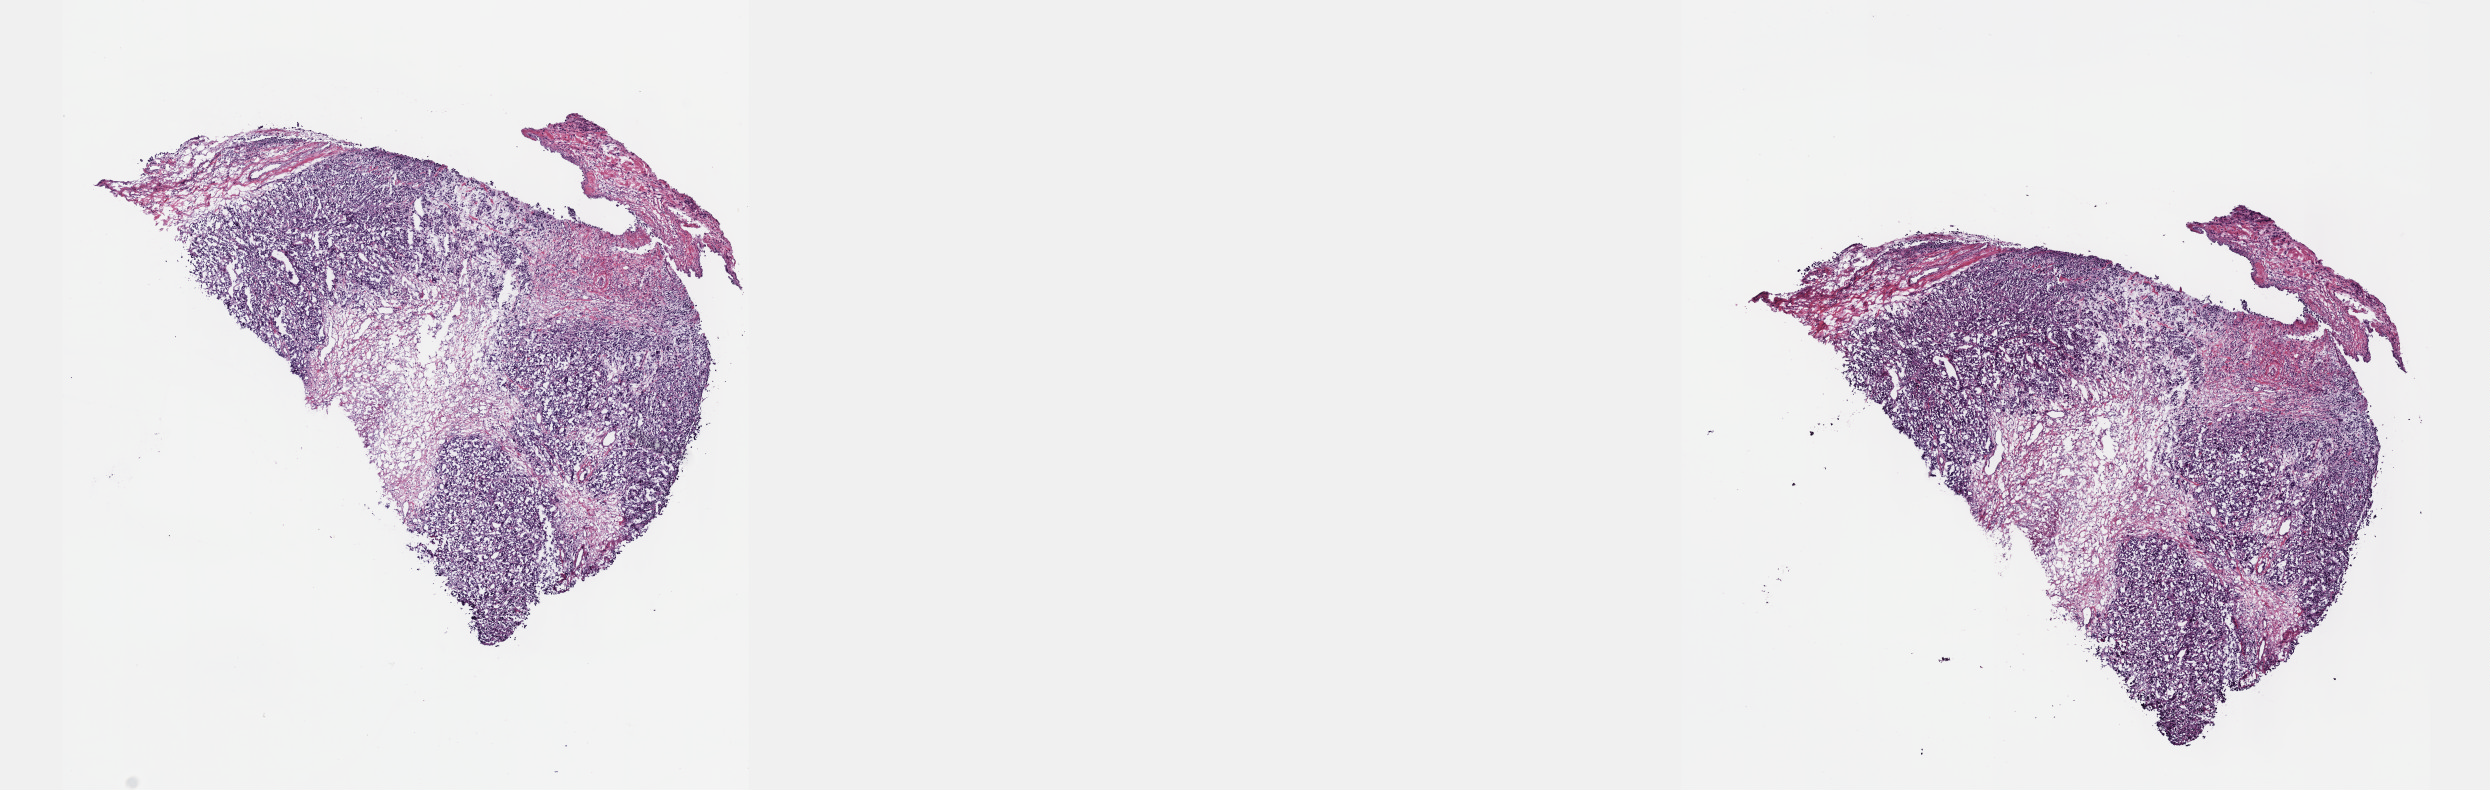
Digitized H&E tissue section (whole slide), low-resolution overview of the scanned area, about 20.1 x 6.4 mm. Frozen section from the top of the tissue portion. Metastatic tumour sample, sampled site: lymph nodes of axilla or arm. Male patient; age at initial diagnosis 85 years. Slide review estimates, as recorded: tumour cells 70%, tumour nuclei 80%, normal cells 0%, stromal cells 15%, necrosis 15%. Infiltration values recorded for this section: lymphocyte infiltration 0%, monocyte infiltration 0%, neutrophil infiltration 0%.
This section: metastatic tumour tissue. Patient diagnosis: Malignant melanoma, NOS.